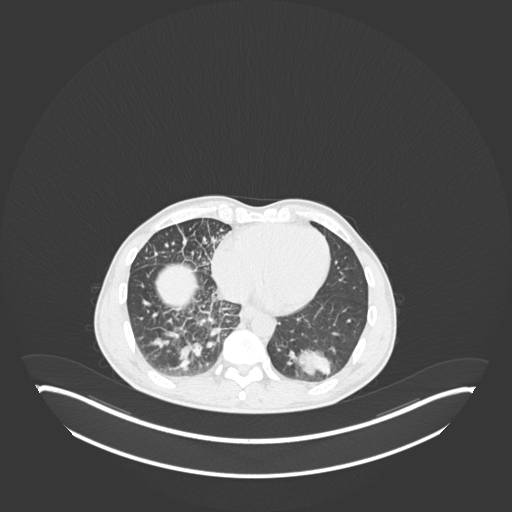
Chest CT, one axial slice; slice 70 of 237 in the series (ordered by position); reconstruction kernel B30f; lung window (W 1500 / L -600 HU); 1 mm slice thickness; 512 × 512 image matrix, field of view 500 × 500 mm. Patient: male, 49 years. Case-level facts recorded for this patient, not image findings: clinical TNM (as recorded): T2b N1 M0.
Outlined on this slice (bounding box drawn by a radiologist):
- lung tumour (recorded histology: adenocarcinoma): bounding box <290,346,338,384> (left, top, right, bottom; pixels)